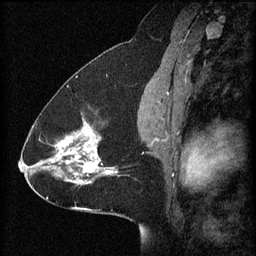
Breast MRI (dynamic contrast-enhanced), one sagittal slice; position 34 of 60 along the scan axis; 3 images stored at this slice position (order not interpretable as contrast timing); 1.5 T; TE 4.2 ms, TR 8.2 ms; 2 mm slice thickness; 256 × 256 image matrix, field of view 200 × 200 mm. Female patient, age 41 years.
Structures marked on this image (semi-automatic segmentation, software-assisted and operator-edited):
- analysis volume of interest (the breast-tissue region the enhancement analysis was run in; not a lesion): bounding box <58,112,124,181> (left, top, right, bottom; pixels)
- tumour enhancement mask (voxels above the 70 % enhancement threshold inside the analysis volume of interest): <58,120,118,181>